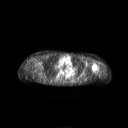
FDG PET of an extremity soft-tissue mass (from a PET/CT study), one axial slice. Position 186 of 267 along the scan axis. 128 × 128 image matrix, field of view 700 × 700 mm. Female patient, age 83 years. From the clinical record (not read from this slice): histological type: pleiomorphic leiomyosarcoma; grade: high; site of the primary tumour: left biceps.
Annotated regions visible in this slice (expert contour drawn on MRI and transferred to this co-registered scan by the dataset authors):
- gross tumour volume including surrounding oedema: bounding box <91,64,97,73> (left, top, right, bottom; pixels)
- gross tumour volume (mass): <93,65,96,69>